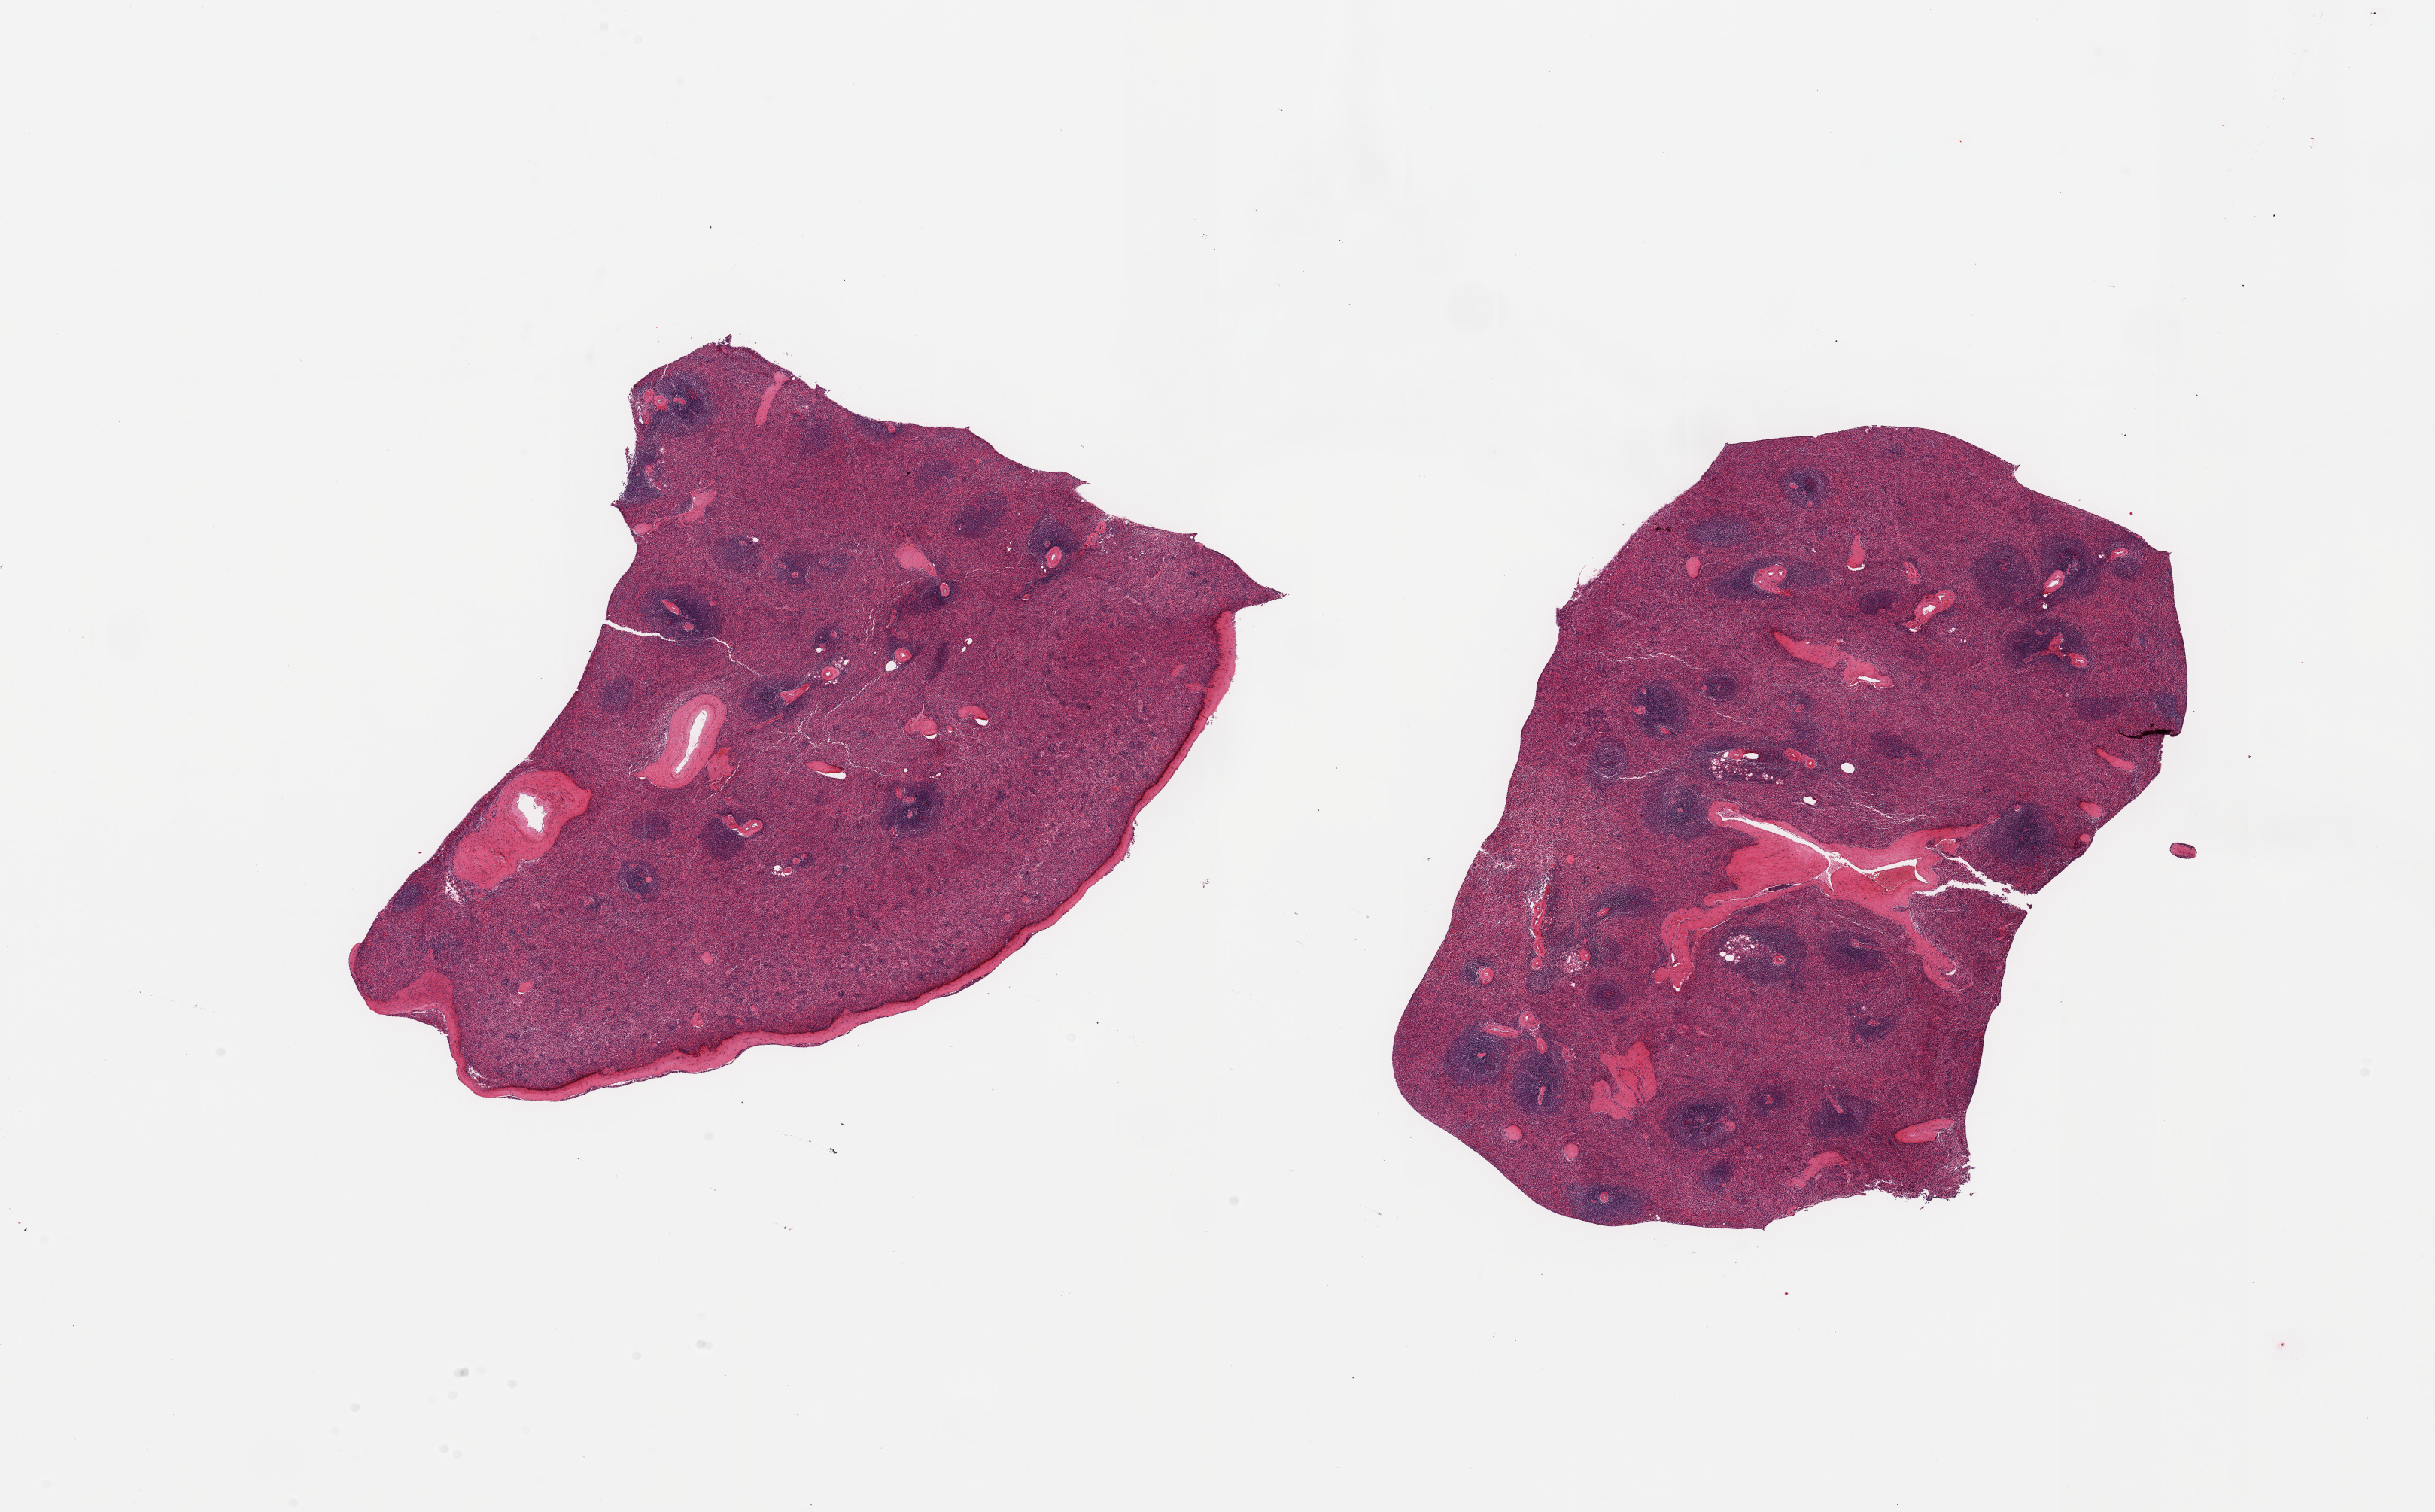
Digitized H&E-stained section, whole scanned area (about 25.6 x 15.9 mm) shown as a low-resolution overview. PAXgene-fixed, paraffin-embedded tissue. Section of spleen (target tissue). Tissue donor sample. Donor sex: male.
Pathologist's review note for this sample: 2 pieces, no significant abnormalities.